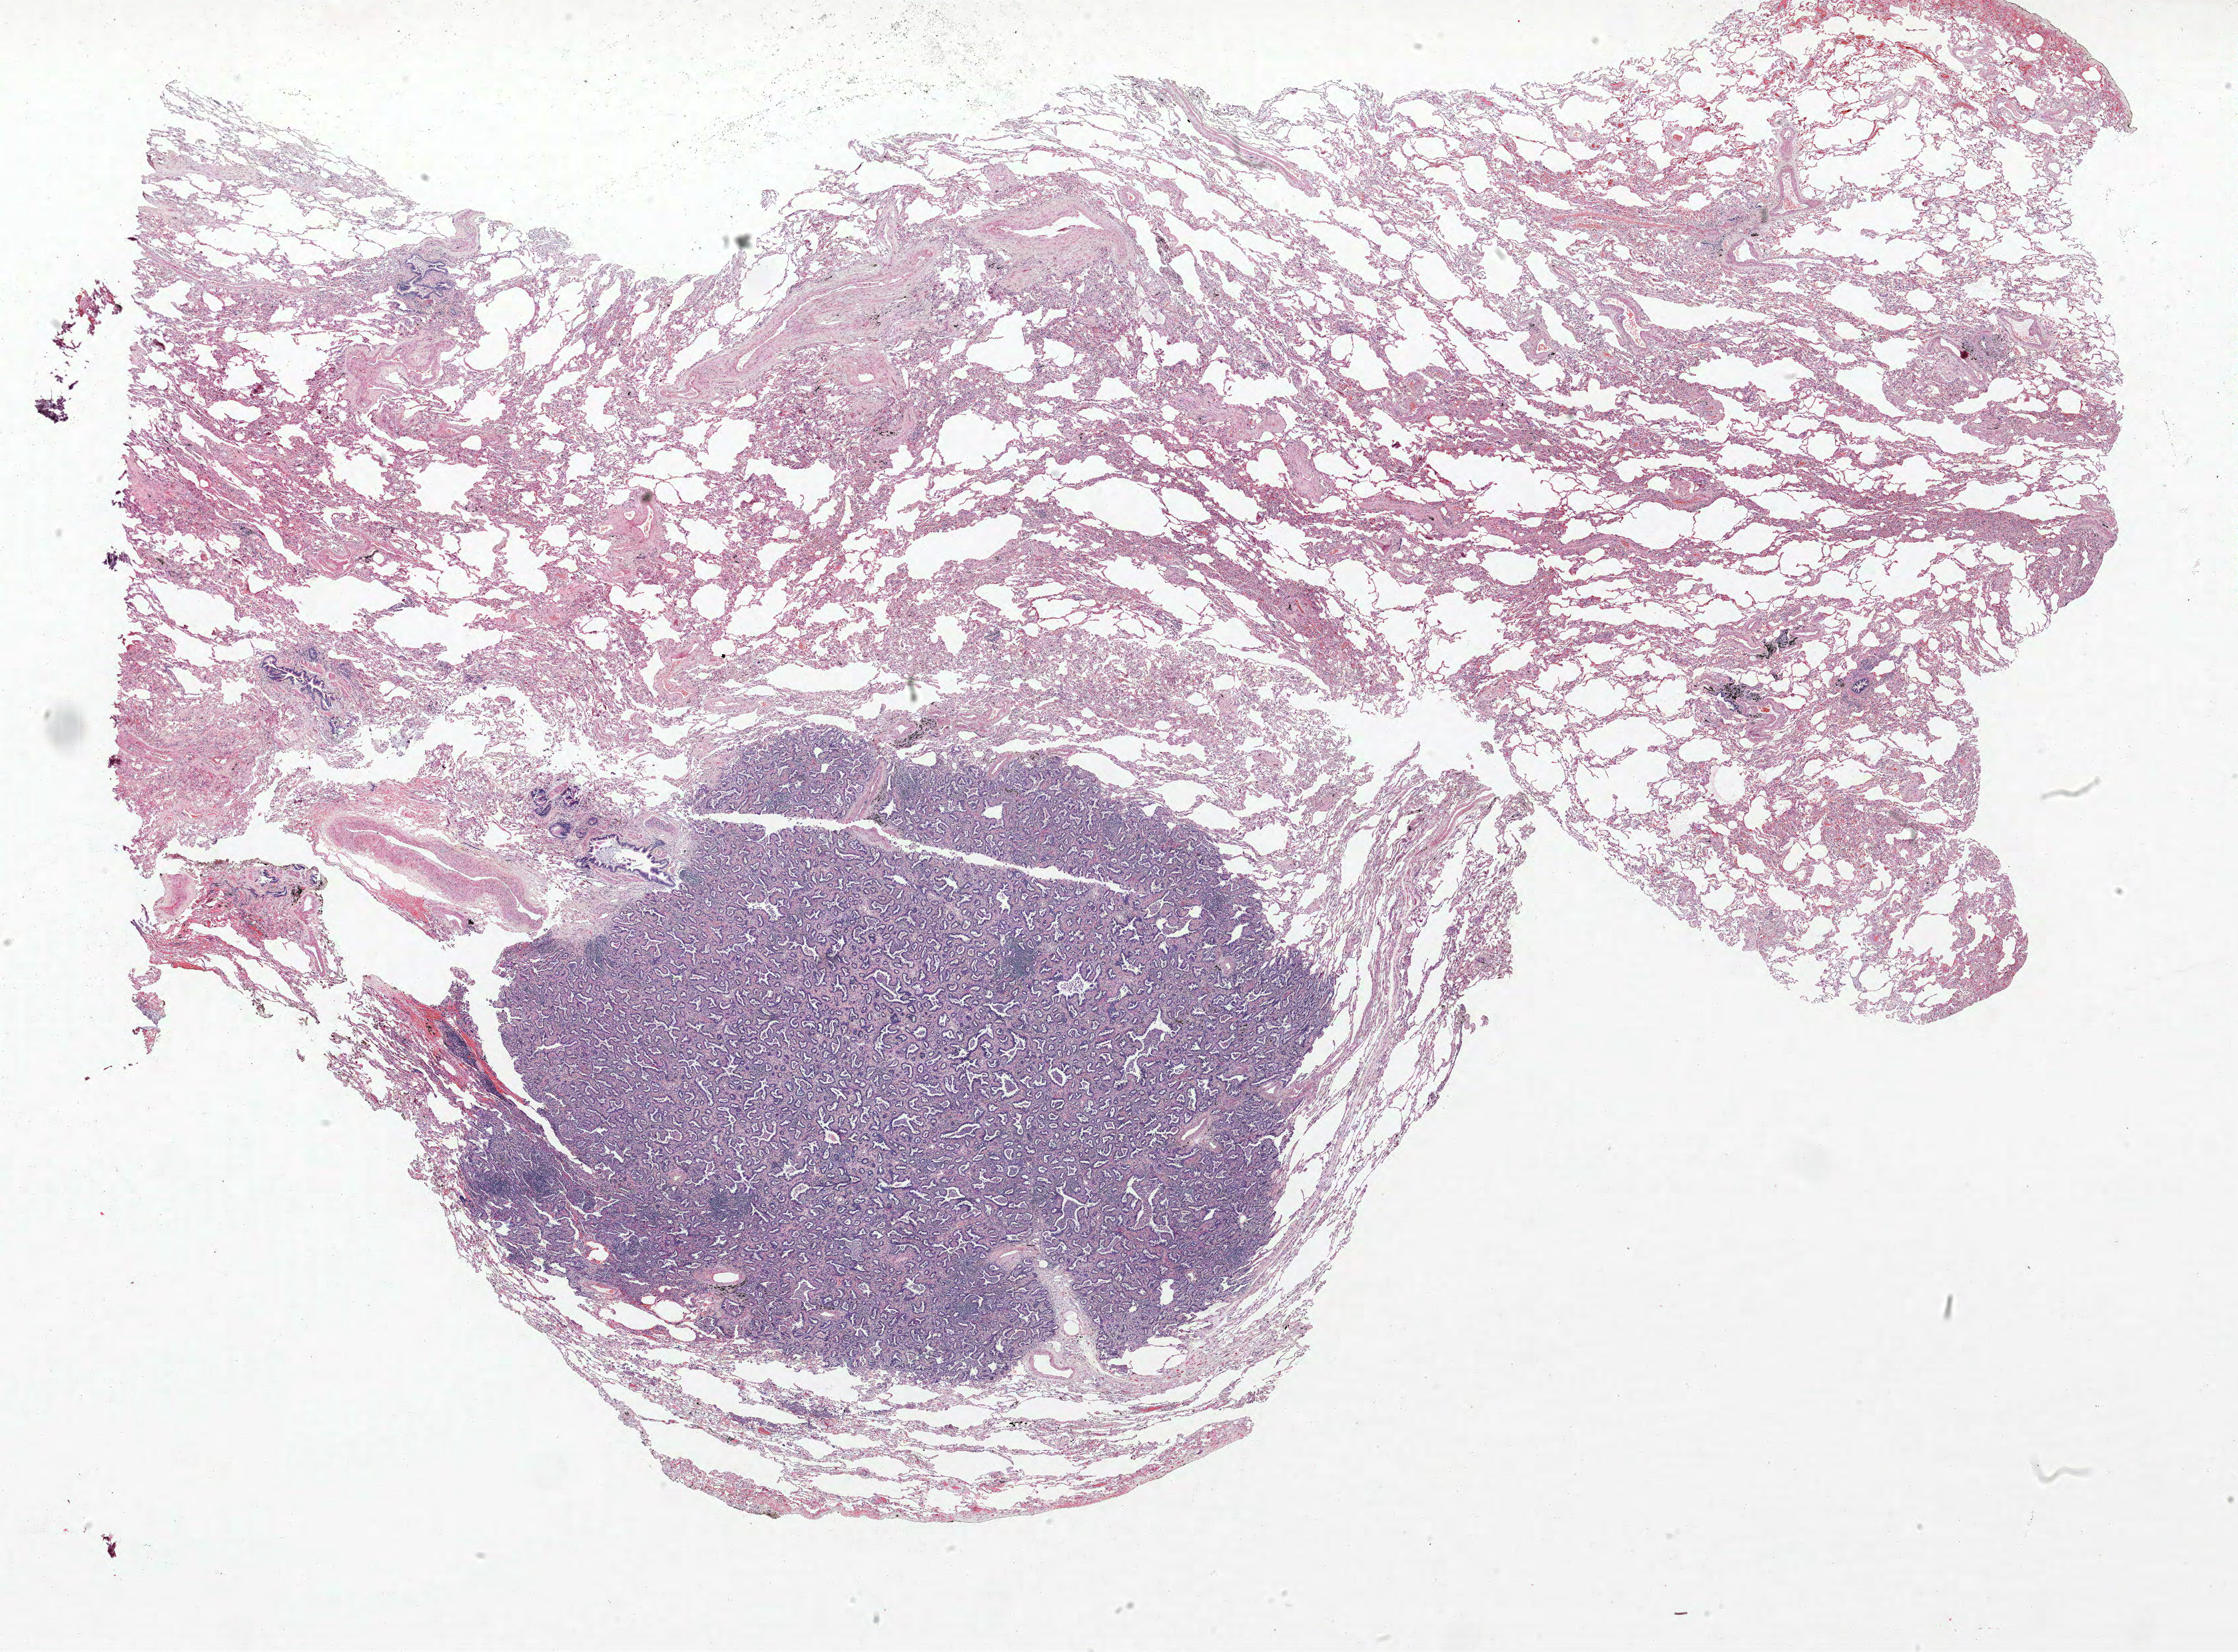
Whole-slide histology image, H&E-stained, whole scanned area (about 26.9 x 19.8 mm) shown as a low-resolution overview, formalin-fixed paraffin-embedded (FFPE) section, lung tissue. Female, age 68 at enrolment. Current smoker at enrolment.
- tumour size (pathology): 12 mm
- primary tumour location (clinical record): left lower lobe
- participant's lung-cancer diagnosis: Bronchiolo-alveolar adenocarcinoma, NOS (ICD-O-3 8250/3)
- stage (AJCC 6th edition): IIIB
- ICD-O-3 topography: lower lobe of lung (C34.3)